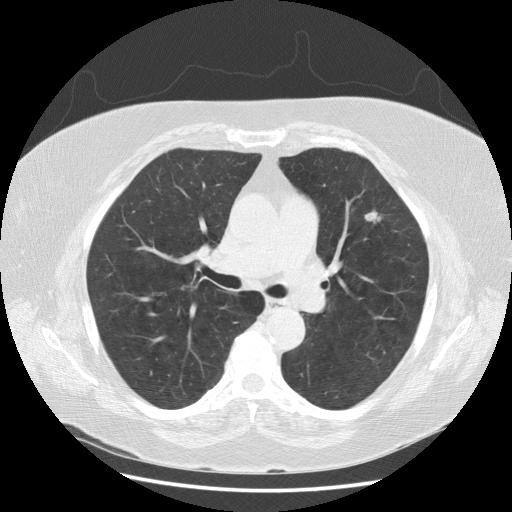
Low-dose screening chest CT, one axial slice; position 99 of 164 along the scan axis; reconstruction kernel STANDARD; lung window (W 1500 / L -600 HU); 2.5 mm slice thickness; 512 × 512 image matrix.
Outlined on this slice (manually delineated by an expert):
- lesion 1 (tumor, upper lobe of left lung): bounding box <365,210,381,223> (left, top, right, bottom; pixels)